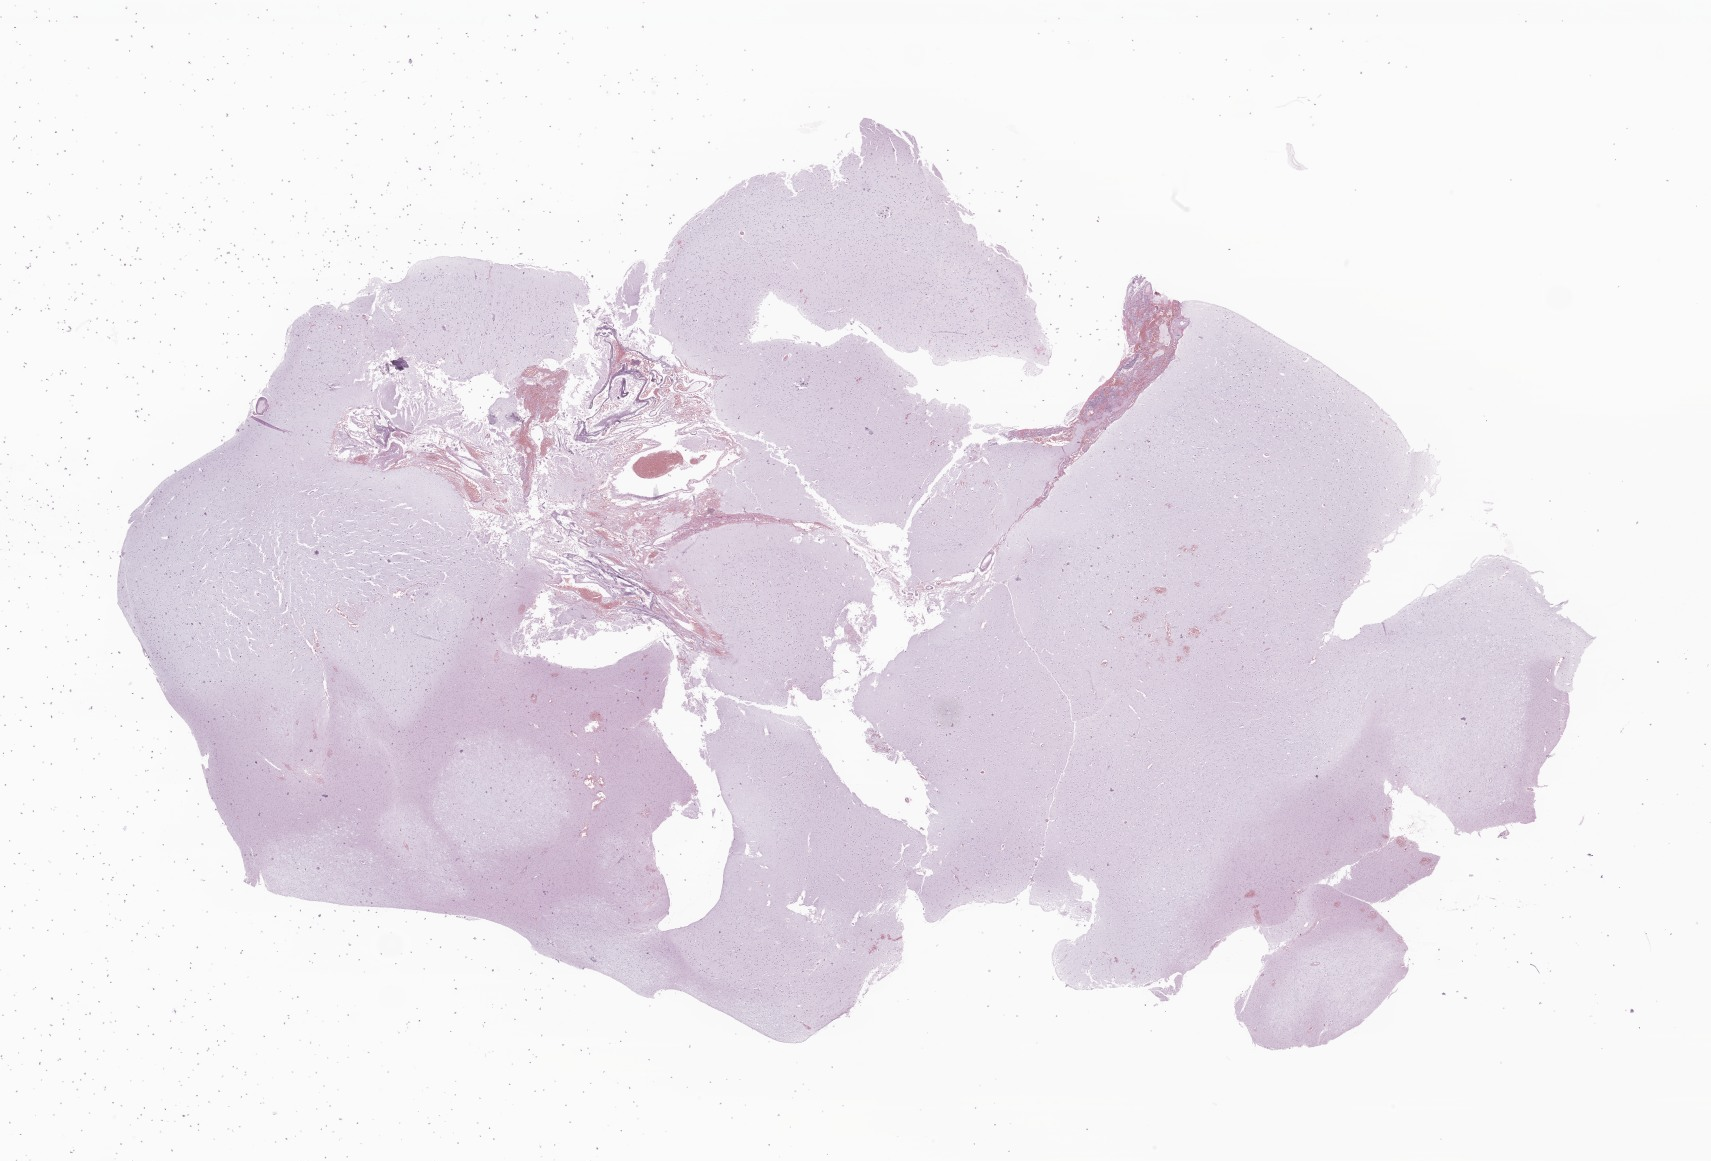
Hematoxylin and eosin (H&E) whole-slide image of tumor tissue from the frontal lobe — whole scanned area (about 28.9 x 19.6 mm) shown as a low-resolution overview, formalin-fixed, paraffin-embedded (FFPE) tissue. Patient male; age 68 months (5 years 8 months).
Recorded diagnosis: Neoplasm, uncertain whether benign or malignant.